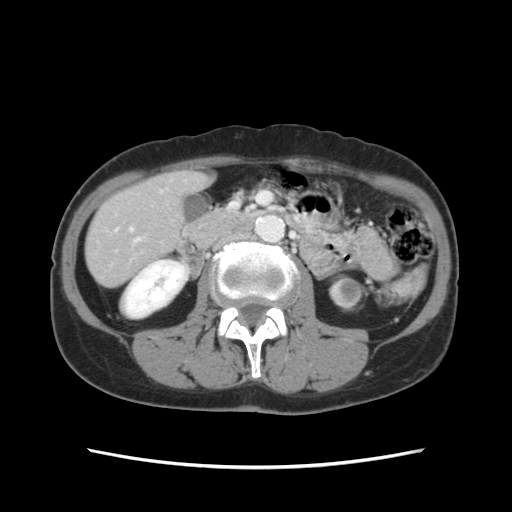
Contrast-enhanced abdominal CT, one axial slice; slice 31 of 120 in the series (ordered by position); intravenous contrast given; soft-tissue window (W 400 / L 40 HU); 512 × 512 image matrix. Female patient, age 70 years. Case-level facts recorded for this patient, not image findings: diagnosis: colorectal cancer liver metastases, imaged before liver resection; multiple liver metastases: no; largest metastasis: 2.5 cm.
Outlined on this slice (expert manual segmentation):
- hepatic veins: box from (x=135, y=239) to (x=139, y=242) px
- liver: (x=87, y=172)–(x=207, y=286)
- planned liver remnant (the part of the liver to remain after resection): (x=87, y=171)–(x=205, y=287)
- portal vein (with intrahepatic branches): (x=130, y=228)–(x=133, y=231)